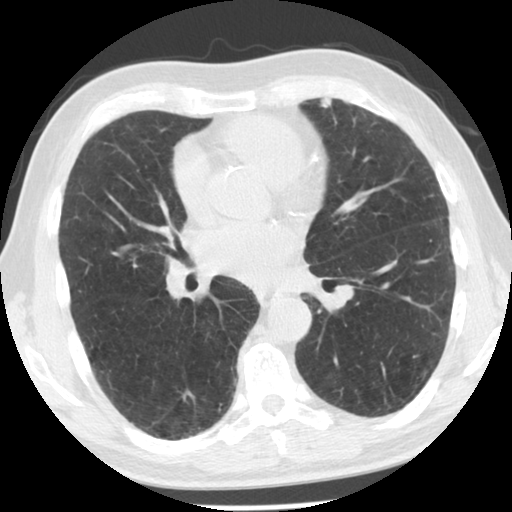
Low-dose screening chest CT, axial slice. Second annual screen. Lung window (W 1500 / L -600 HU). 2.5 mm slice thickness. 140 kVp. 512 × 512 image matrix, field of view 330 × 330 mm. Male, age 66 years at enrolment.
• Lesion marked by an expert reader, box from (x=306, y=89) to (x=347, y=127) px.
• The exam's reader record, not a measurement of the box and not confirmed to be the same lesion: non-calcified nodule or mass ≥4 mm, lingula, 6 × 5 mm, smooth margins, soft tissue attenuation, pre-existing on the prior screen: yes; interval growth: yes.
• Later outcome: lung cancer diagnosed 148 days after this screen — adenocarcinoma, NOS, left upper lobe, moderately differentiated (G2), stage IIB (AJCC 6th edition), 9 mm at pathology.